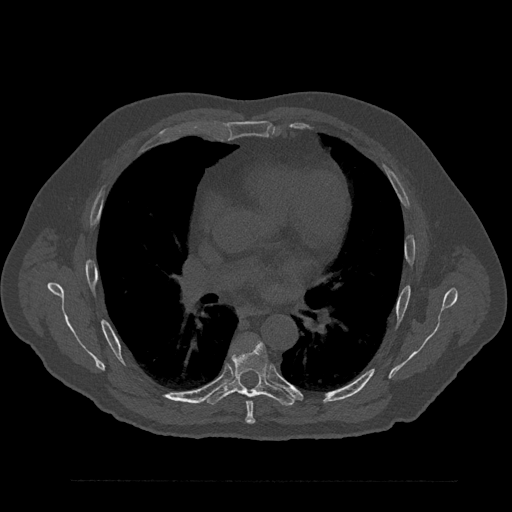
CT including the spine, one axial slice. Reconstruction kernel Br40s/3. 120 kVp. Bone window (W 1800 / L 400 HU). 0.5 mm slice thickness. 512 × 512 image matrix, field of view 430 × 430 mm. Male patient, age 61 years. From the clinical record (not read from this slice): primary cancer: prostate.
Annotated regions visible in this slice (semi-automatically segmented with operator editing):
- T6 vertebra: box from (x=245, y=401) to (x=255, y=424) px
- T7 vertebra: (x=204, y=339)–(x=295, y=406)